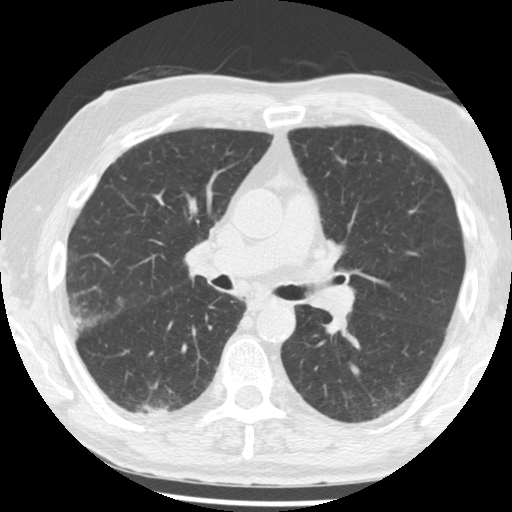
Low-dose screening chest CT, one axial slice. 120 kVp. Lung window (W 1500 / L -600 HU). 2.5 mm slice thickness. 512 × 512 image matrix.
Structures marked on this image (outlined manually by an expert reader):
- lesion 1 (tumor, lower lobe of right lung): bounding box <133,405,174,418> (left, top, right, bottom; pixels)